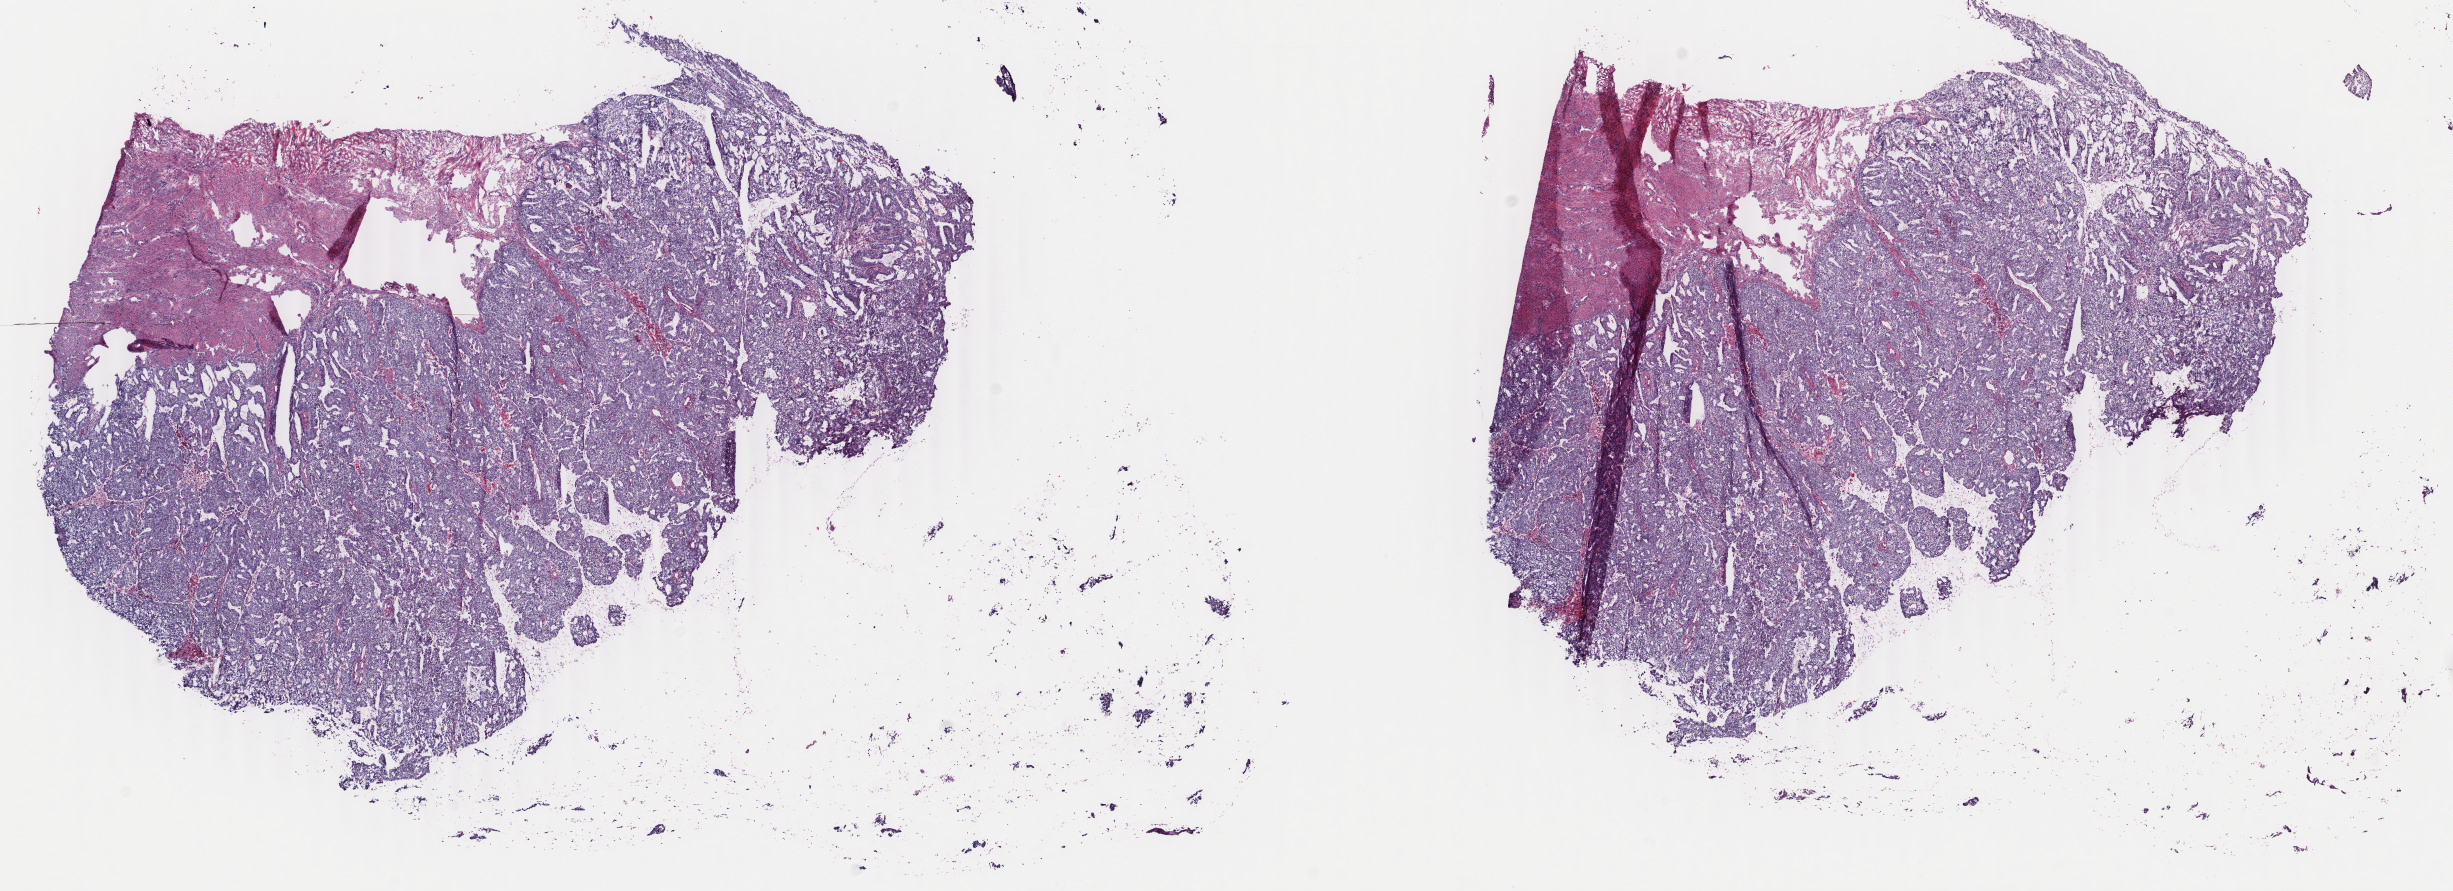
H&E whole-slide image, whole scanned area (about 19.5 x 7.1 mm, from a 40x scan) shown as a low-resolution overview, frozen section, primary tumour sample from the uterus. Patient: female, age at initial diagnosis 34 years. Histologic grade: G2 (moderately differentiated). Composition of this section per pathologist review: tumour cells 70%, tumour nuclei 80%, normal cells 20%, stromal cells 0%, necrosis 10%. Inflammatory infiltration, as recorded: lymphocyte infiltration 10%, monocyte infiltration 0%, neutrophil infiltration 10%.
Diagnosis: Endometrioid adenocarcinoma, secretory variant (endometrium). FIGO stage: IB.